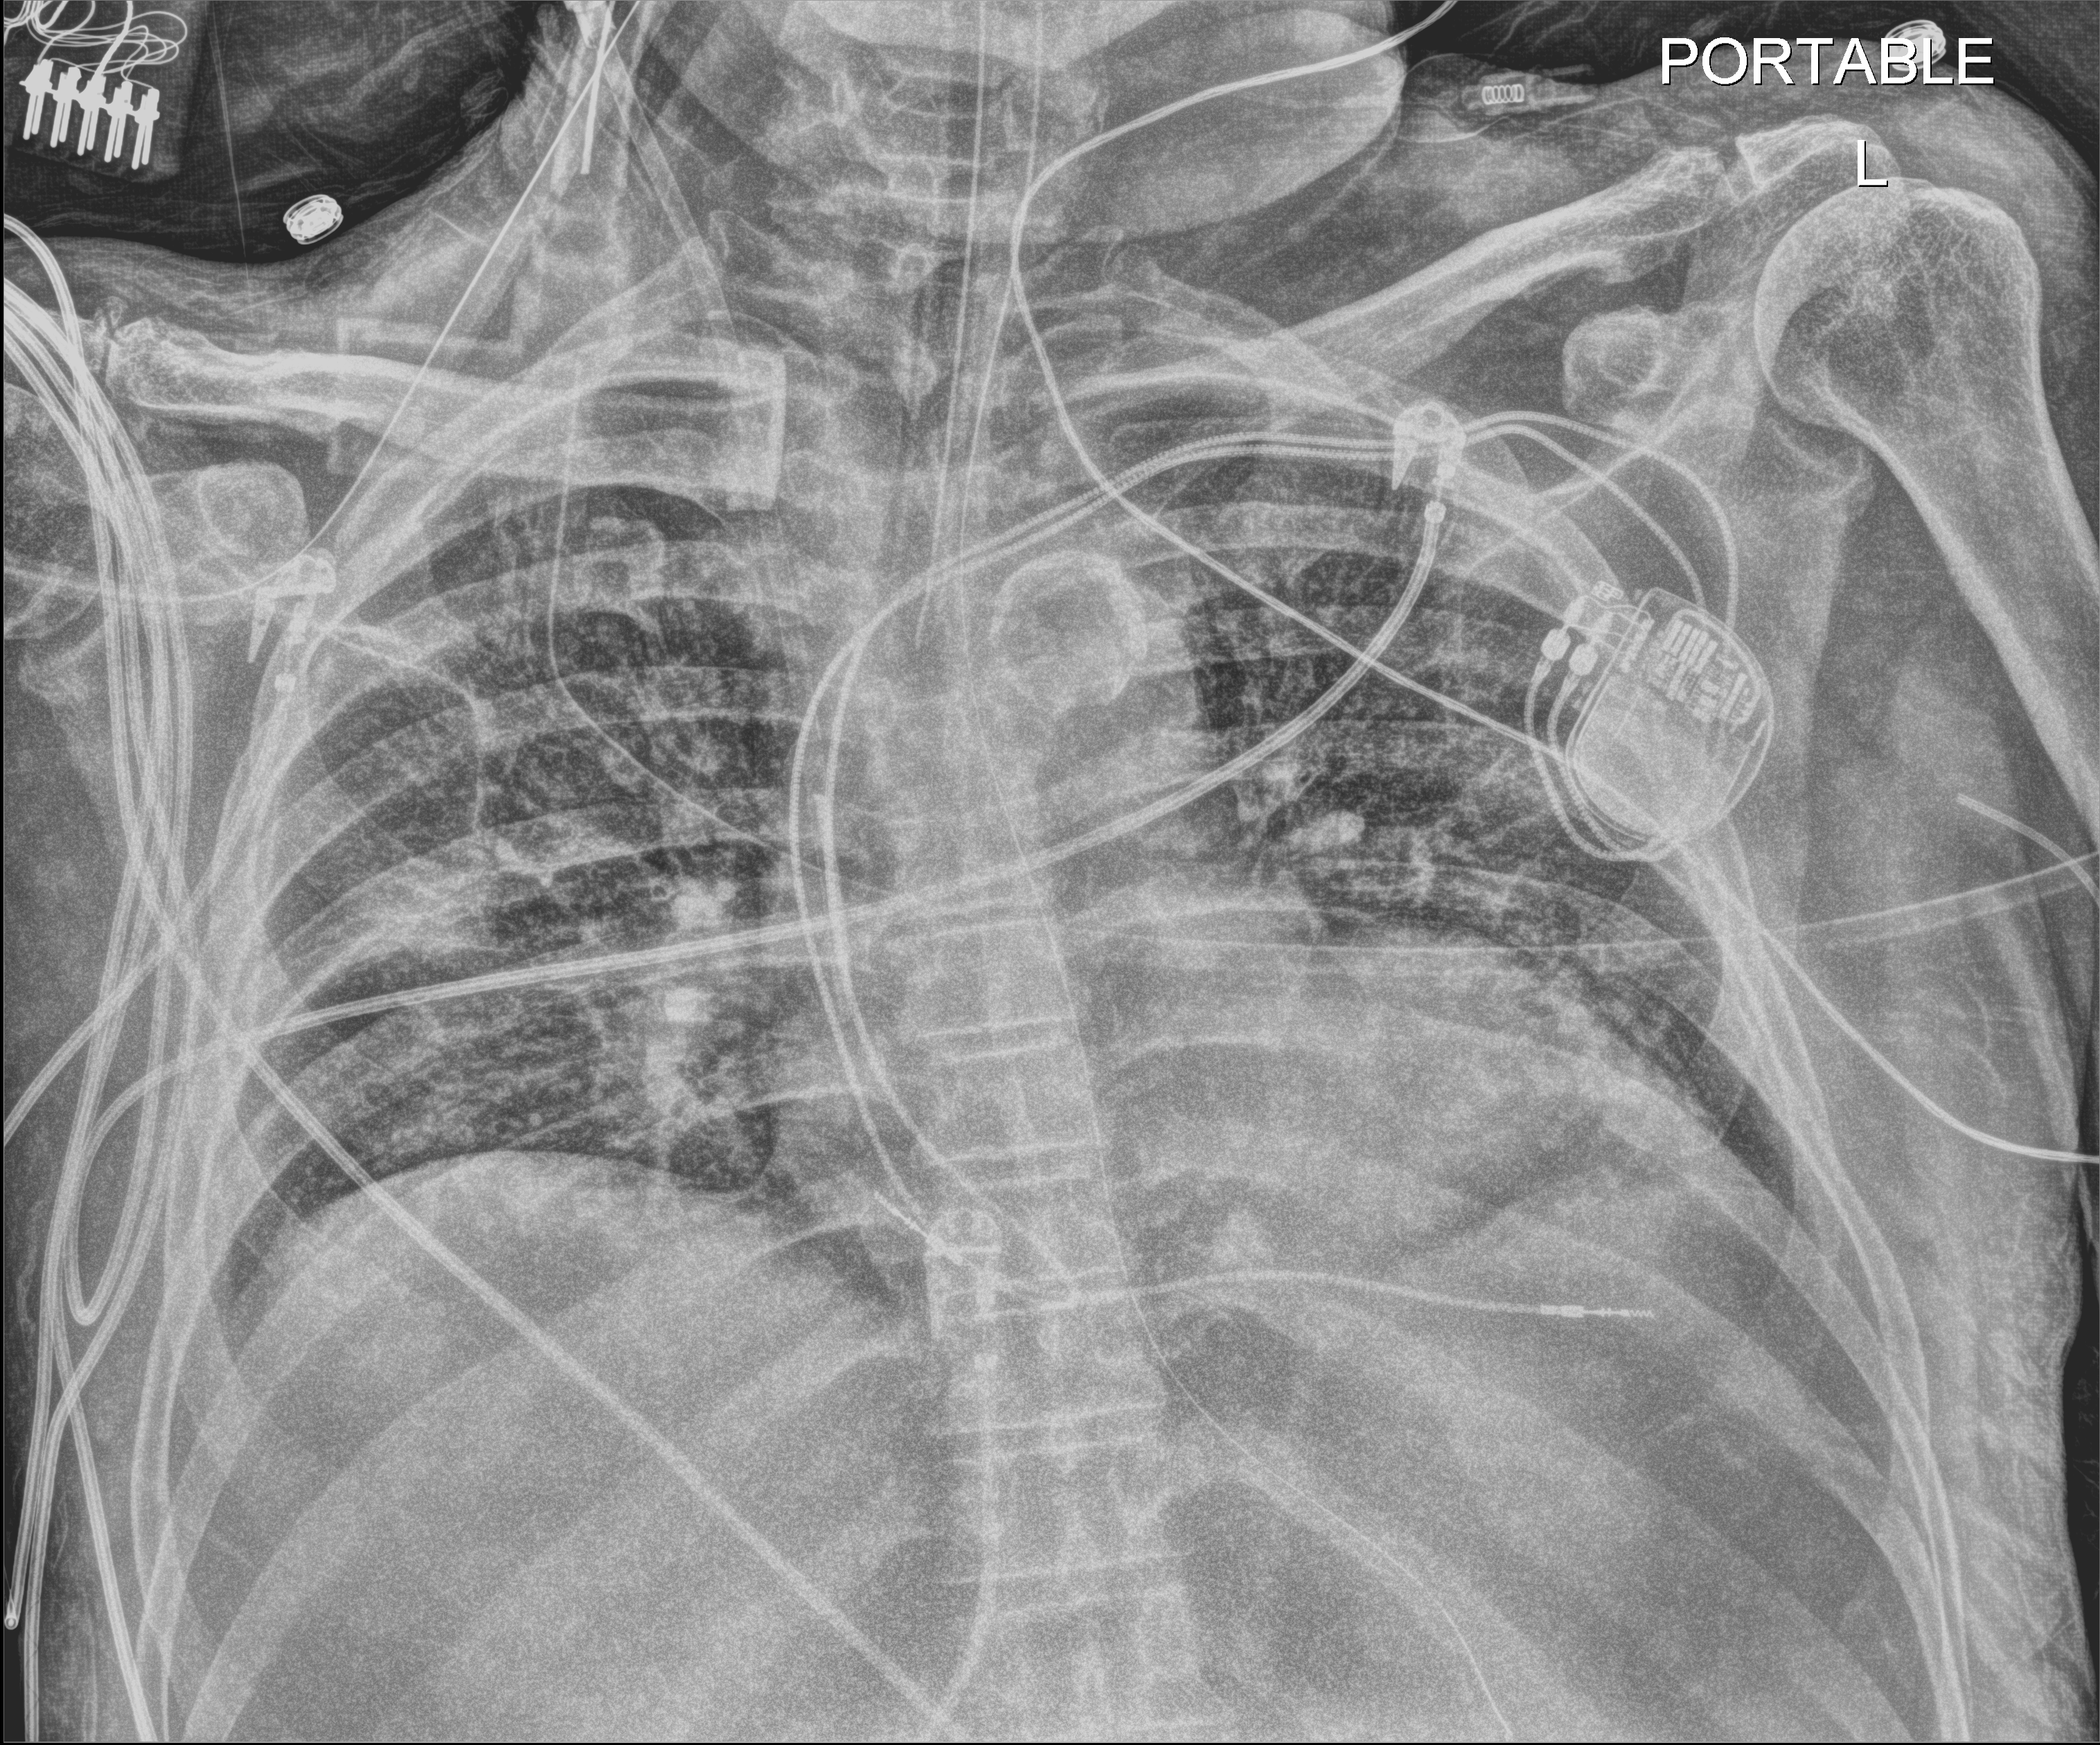
Chest X-ray (portable). Male patient hospitalised with COVID-19, age 60–74 years.
Admission-level facts for this patient (not findings on this image; timing relative to this image not recorded):
- mechanically ventilated during this hospital stay: yes